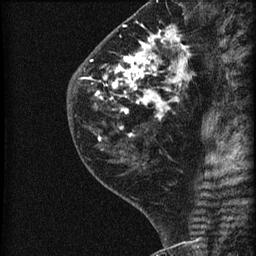
Breast MRI (dynamic contrast-enhanced), one sagittal slice; position 25 of 60 along the scan axis; dynamic contrast-enhanced series, image 2 of 3 at this slice position (ordered by acquisition); 1.5 T; TE 4.2 ms, TR 22.7 ms; 1.8 mm slice thickness; 256 × 256 image matrix, field of view 180 × 180 mm. Patient: female, 45 years. From the clinical record (not read from this slice): setting: breast cancer imaged before/during neoadjuvant chemotherapy; receptor status: HR-positive, HER2-negative.
Structures marked on this image (semi-automatically segmented with operator editing):
- analysis volume of interest (the breast-tissue region the enhancement analysis was run in; not a lesion): box from (x=74, y=11) to (x=205, y=140) px
- tumour enhancement mask (voxels above the 90 % enhancement threshold inside the analysis volume of interest): (x=91, y=27)–(x=190, y=135)